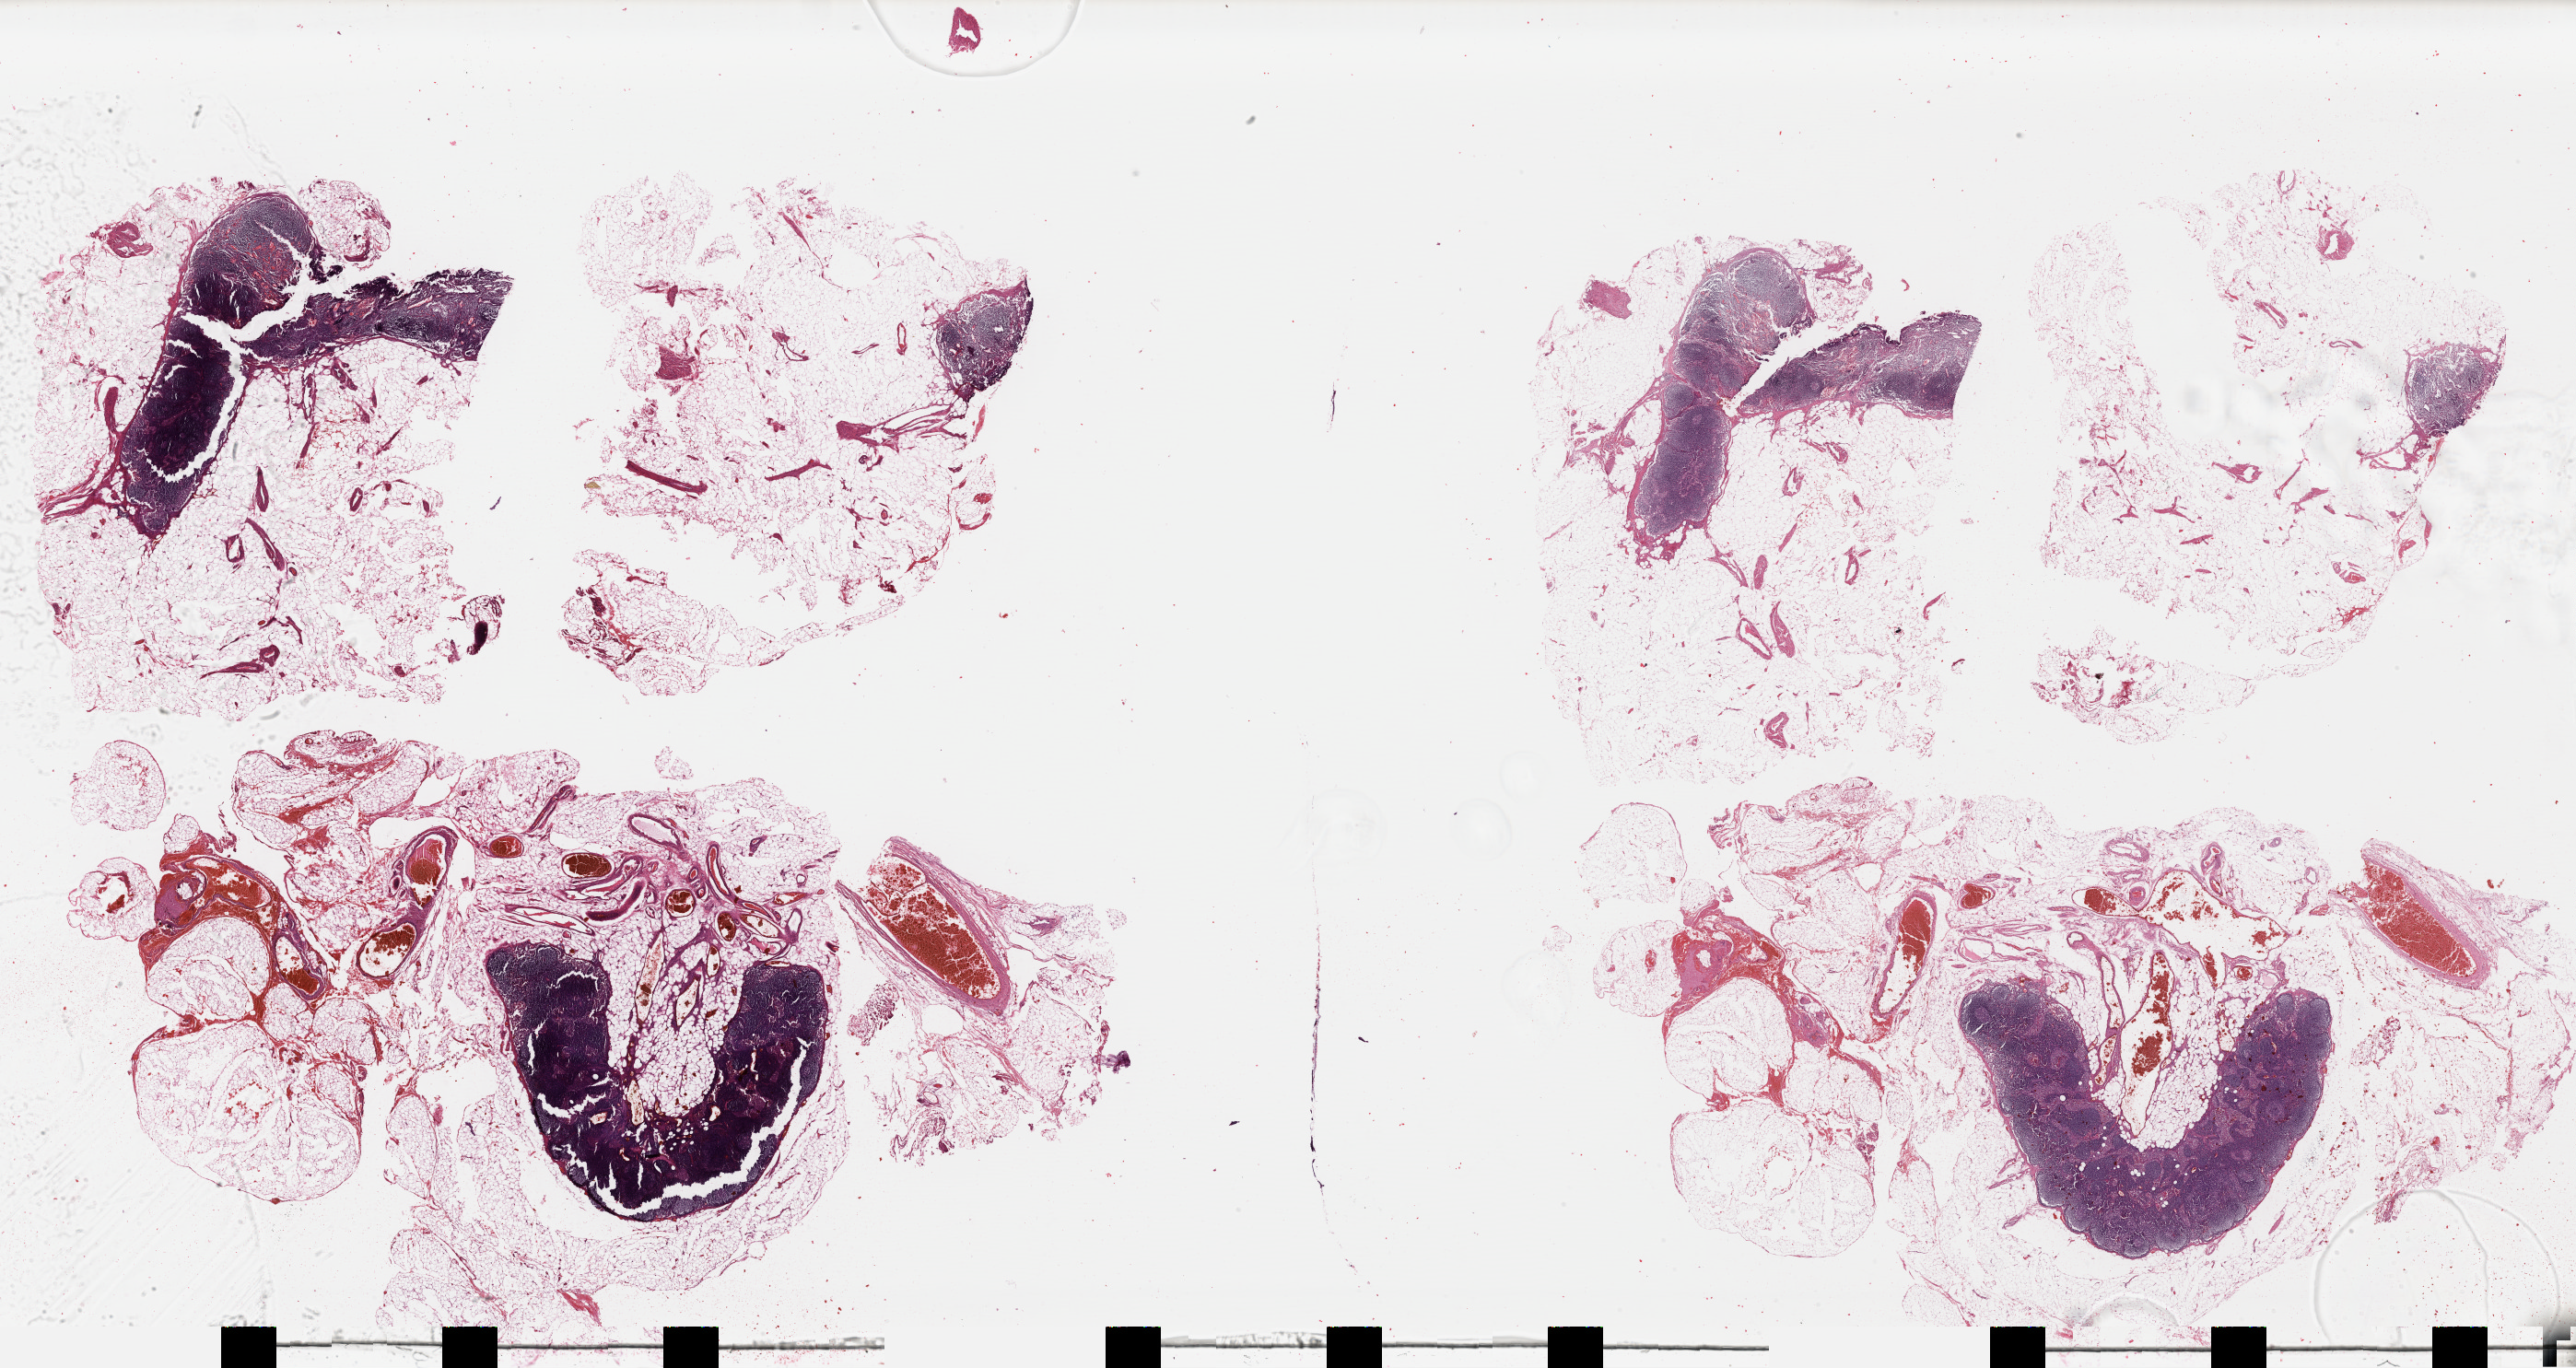
Whole-slide histology image, H&E, whole scanned area (about 44.0 x 23.3 mm, from a 40x scan) shown as a low-resolution overview; formalin-fixed paraffin-embedded (FFPE) diagnostic section; metastatic tumour sample, sampled site: lymph node. Male patient; age at initial diagnosis 65 years.
This section: metastatic tumour tissue. Patient diagnosis: Malignant melanoma, NOS.